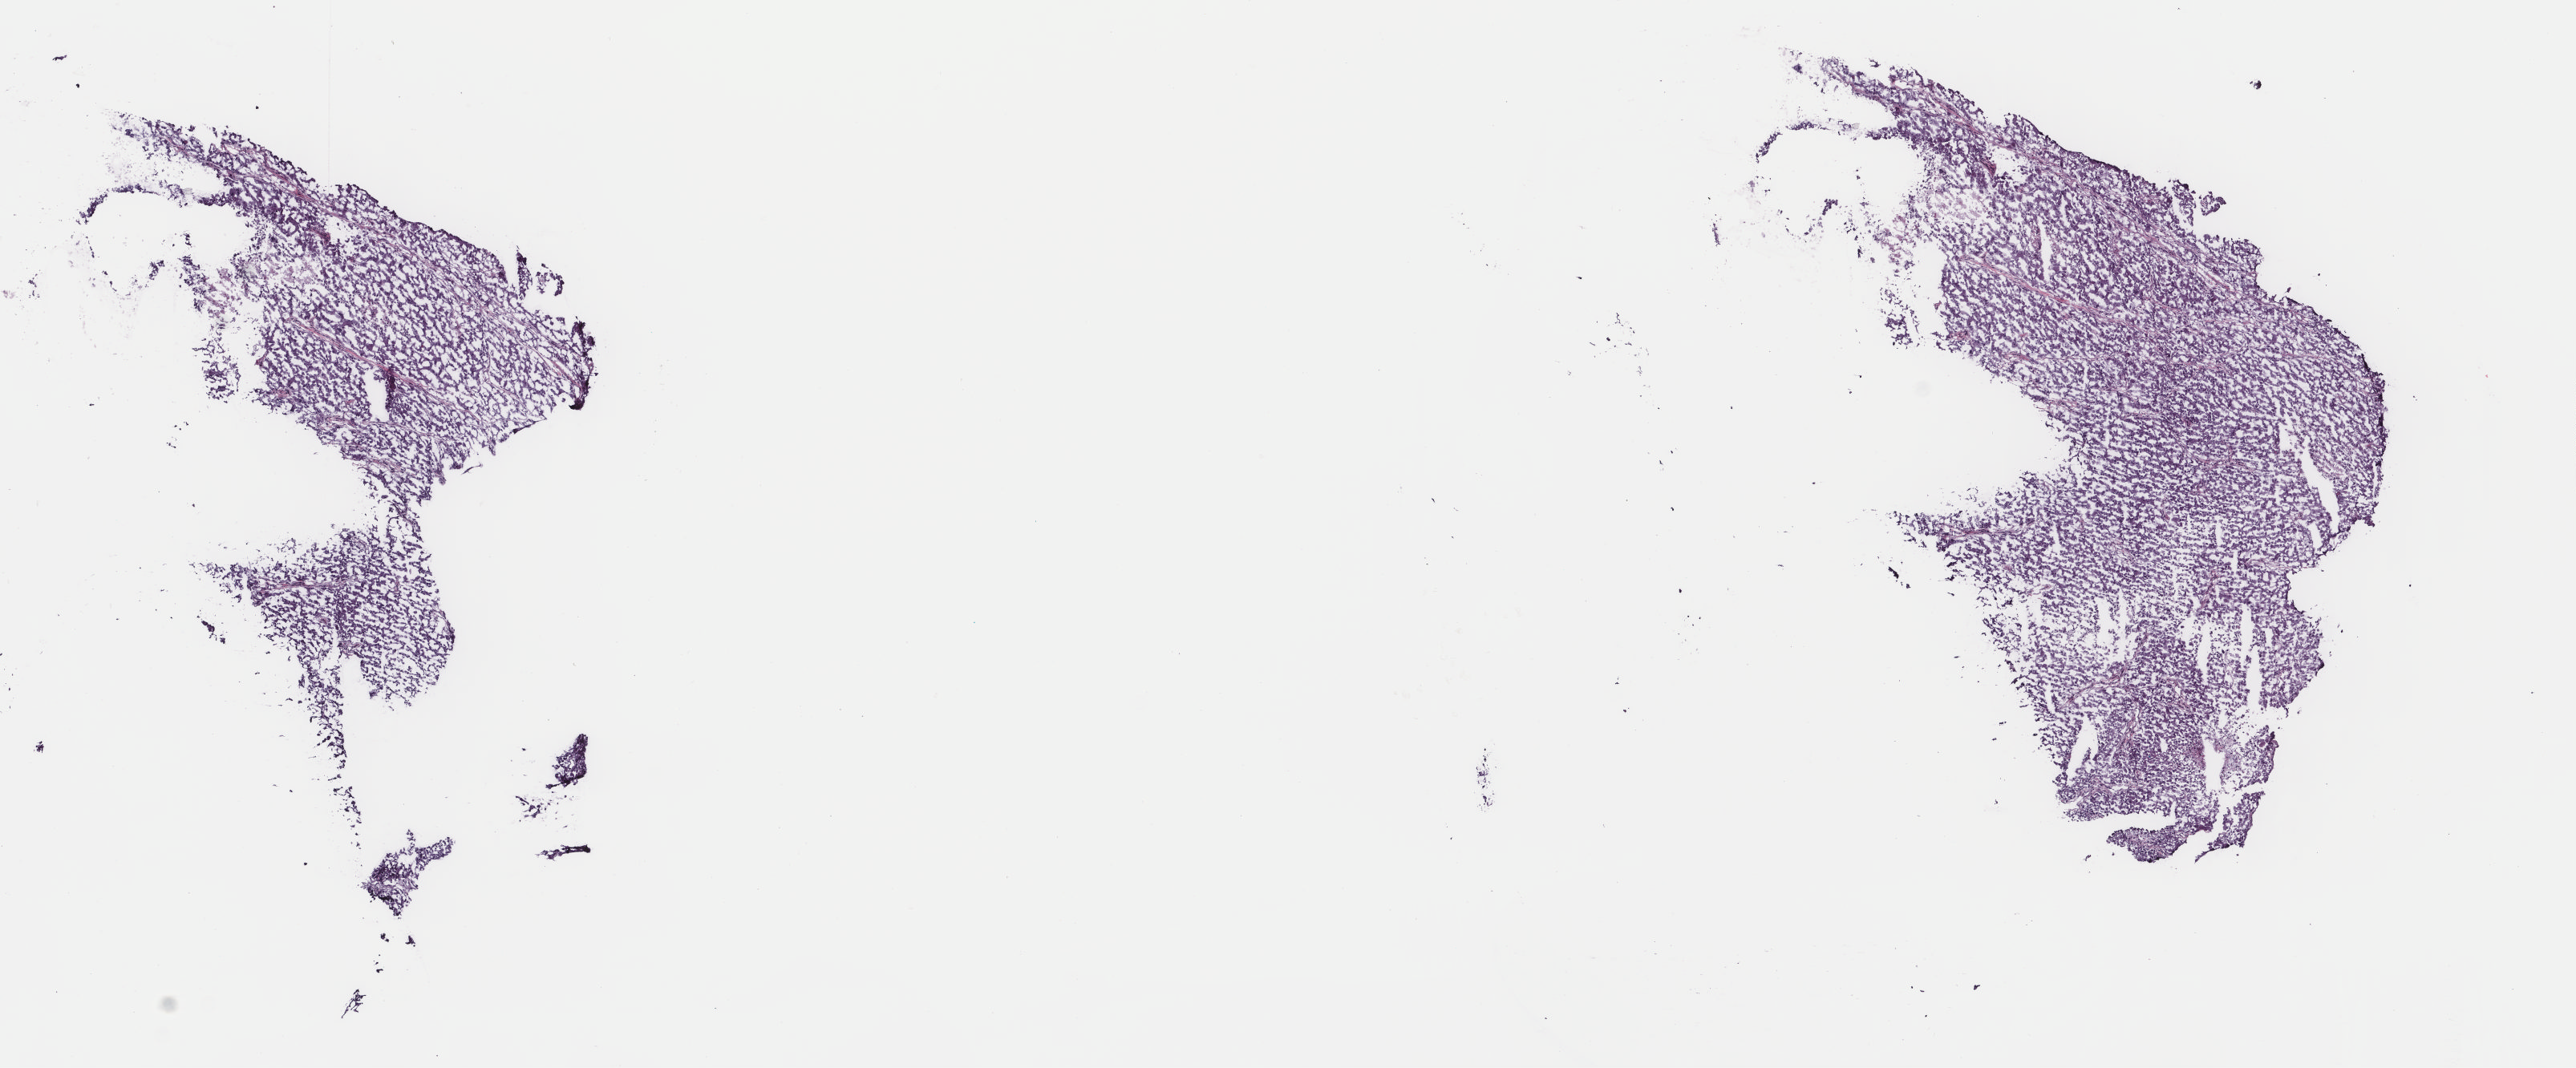
Digitized H&E-stained tissue section (whole slide) — whole scanned area (about 12.7 x 5.3 mm, acquisition: 40x scan) shown as a low-resolution overview; frozen section; adrenal cortex, primary tumour sample. Female patient; age at initial diagnosis 23 years. Composition of this section per pathologist review: tumour cells 100%, tumour nuclei 80%, normal cells 0%, stromal cells 0%, necrosis 0%. Inflammatory infiltration, as recorded: lymphocyte infiltration 1%, monocyte infiltration 0%, neutrophil infiltration 0%.
Lymph nodes positive (case pathology): 52 of 52 examined. Diagnosis: Adrenal cortical carcinoma.